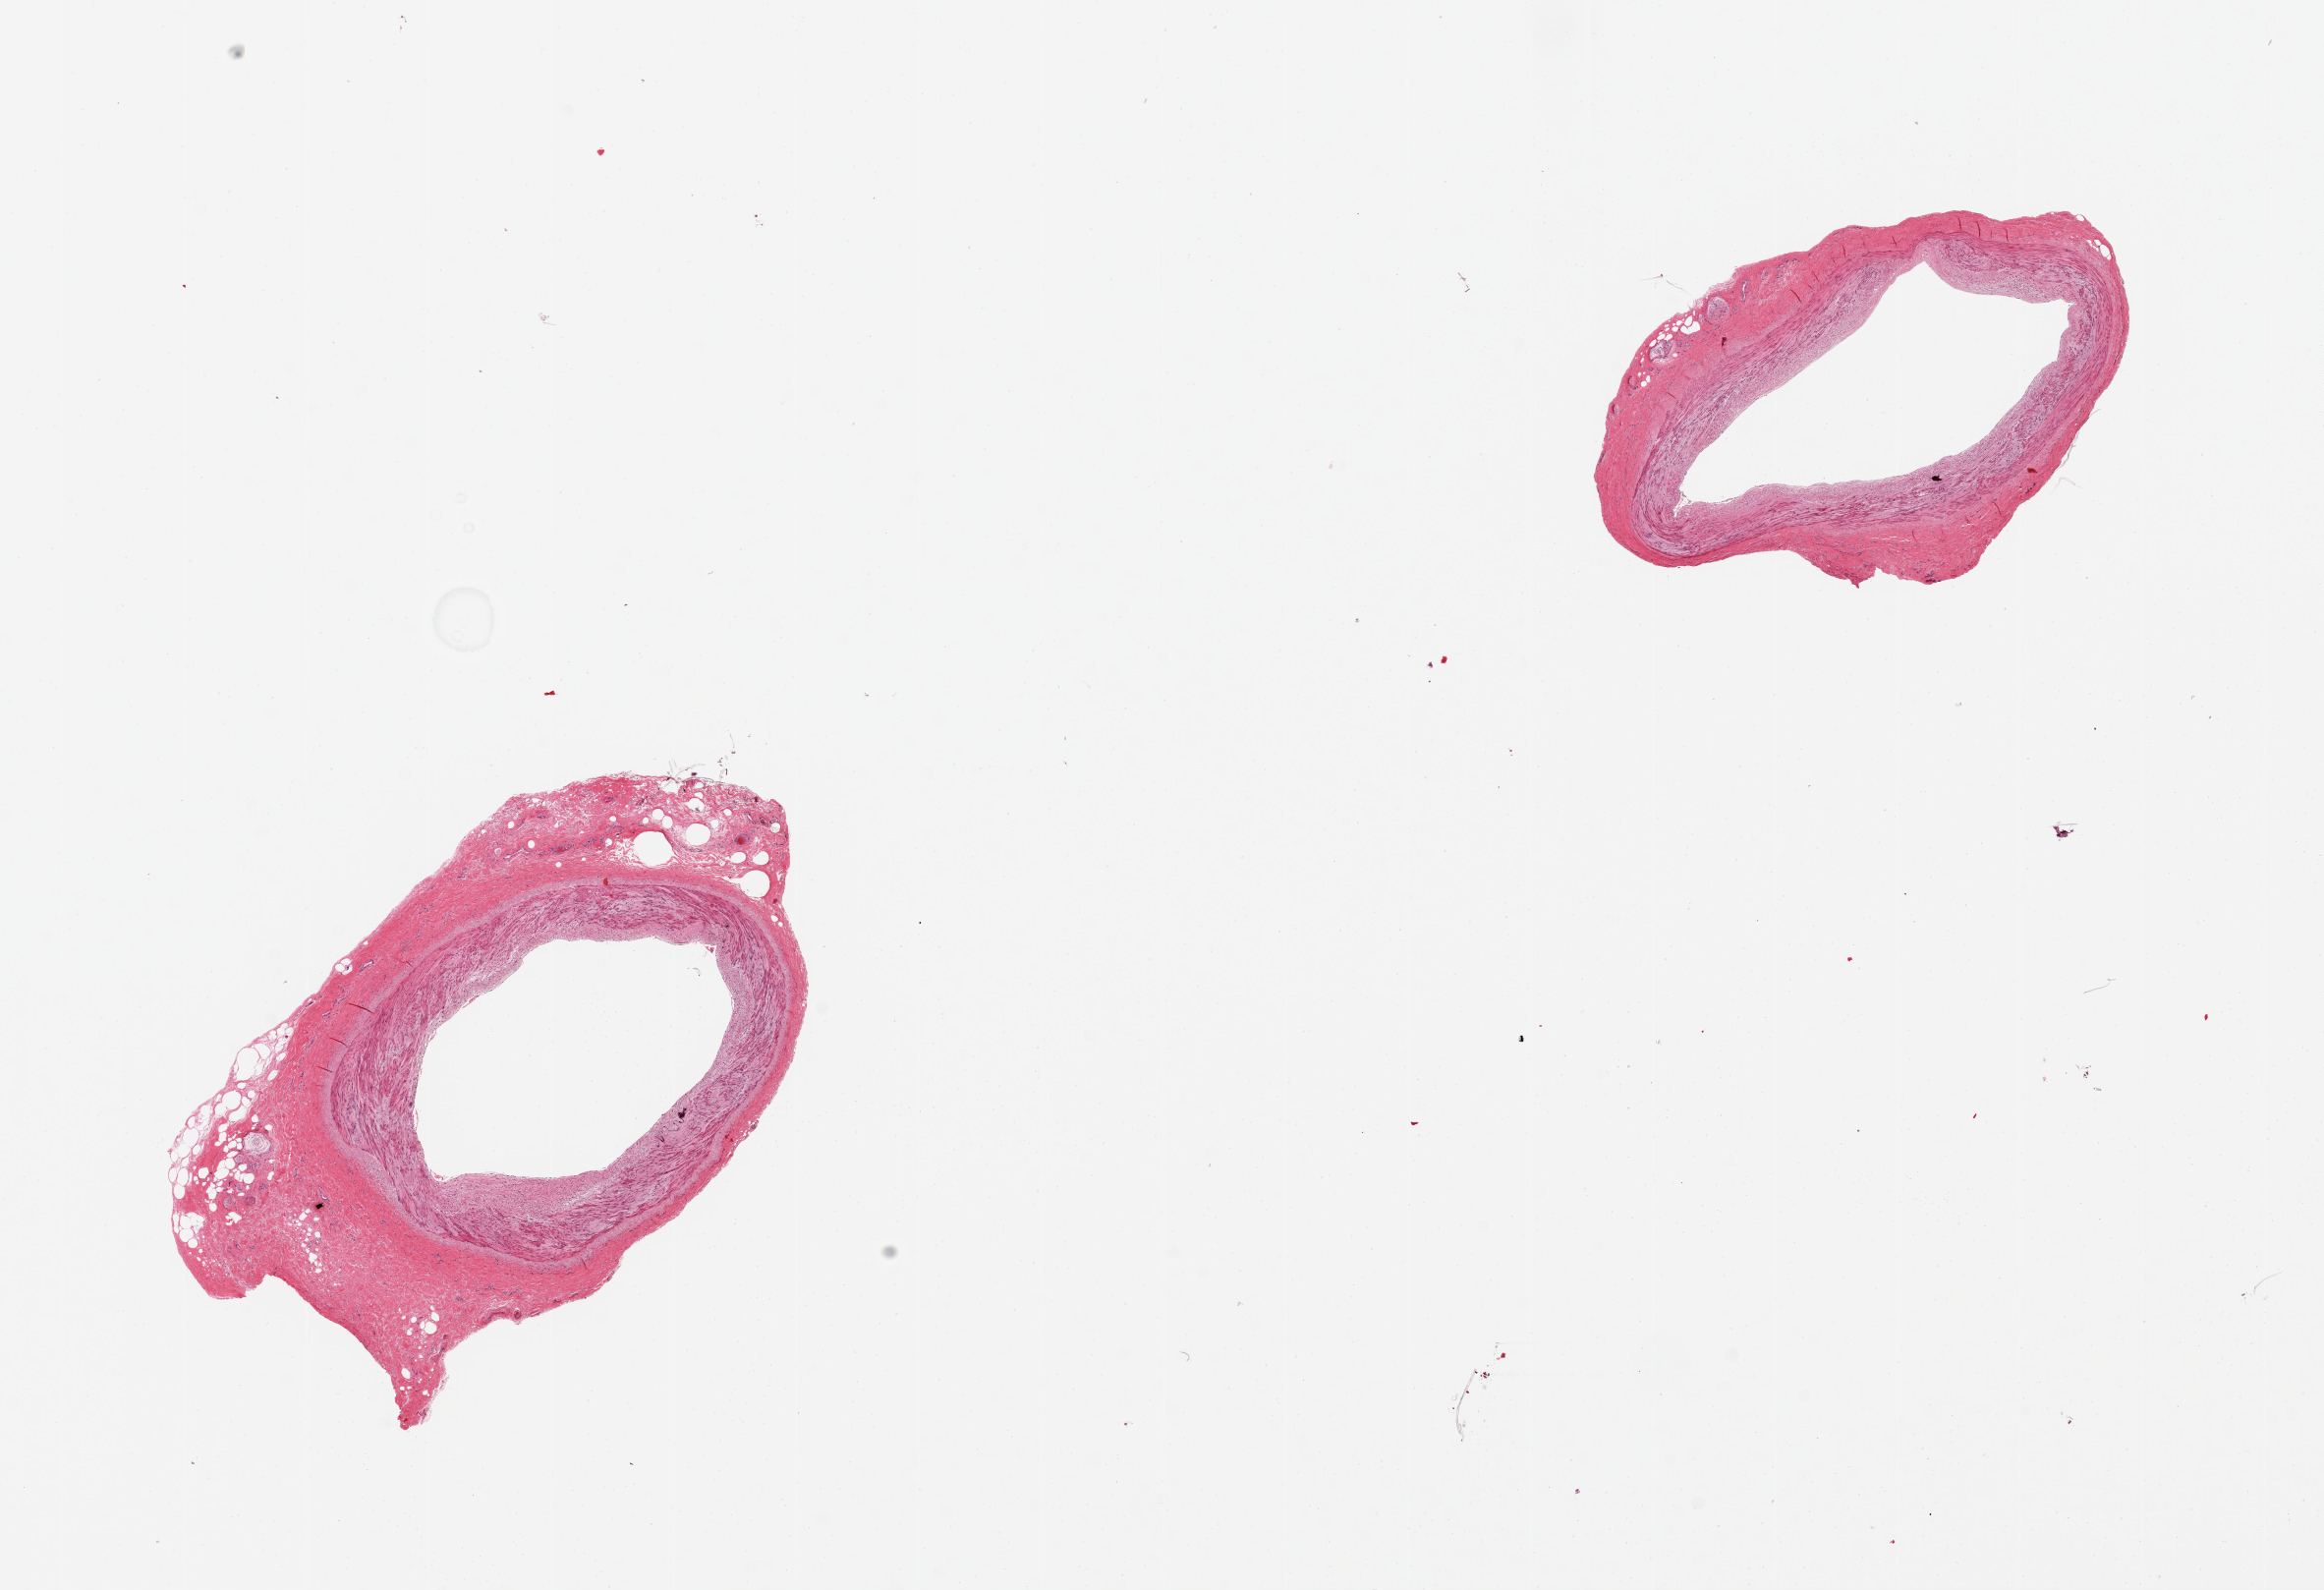
Whole-slide image, haematoxylin and eosin stain, brightfield, whole scanned area (about 18.7 x 12.8 mm, acquisition: 20x scan) shown as a low-resolution overview. Donor: female.
Specimen: PAXgene-fixed paraffin-embedded (PFPE) section; sampled site (target tissue): tibial artery; tissue donor sample.